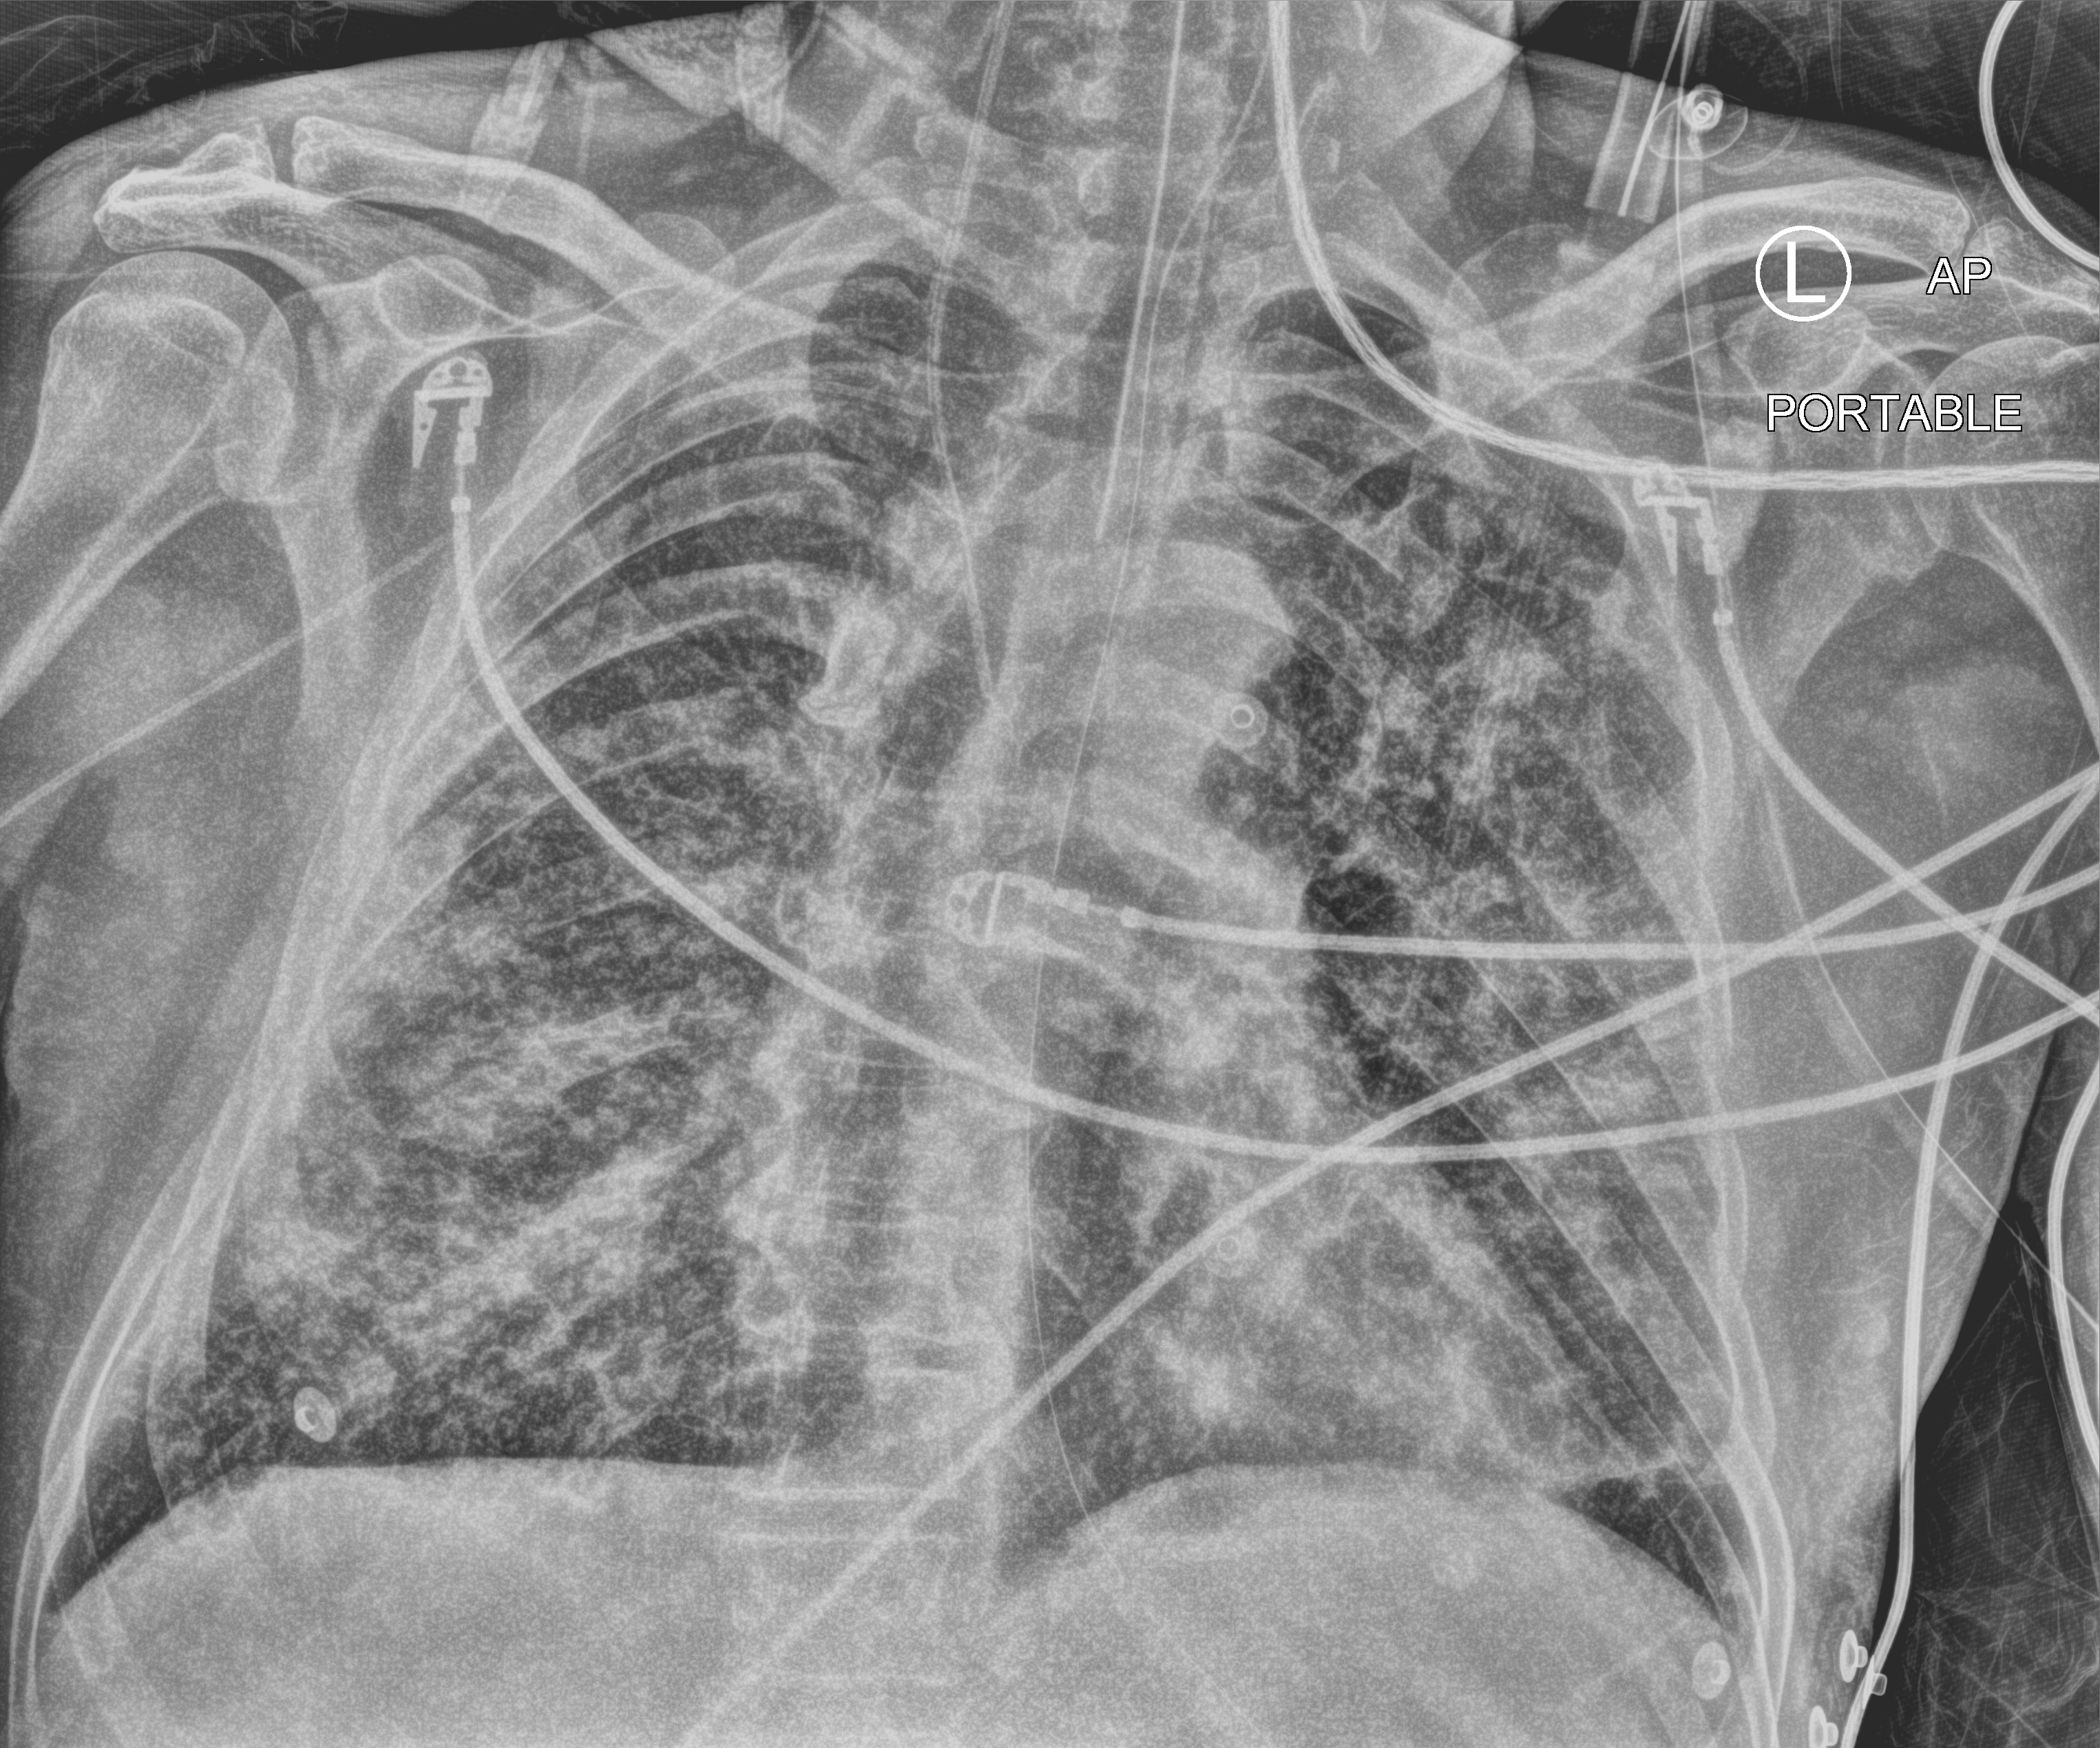
Portable chest radiograph, anteroposterior (AP) projection. Patient hospitalised with COVID-19; male, aged 60–74 years.
Hospital-stay facts (about this admission, not read from this image; timing relative to this image not recorded): hypertension (admission record): yes; mechanically ventilated during this hospital stay: yes.